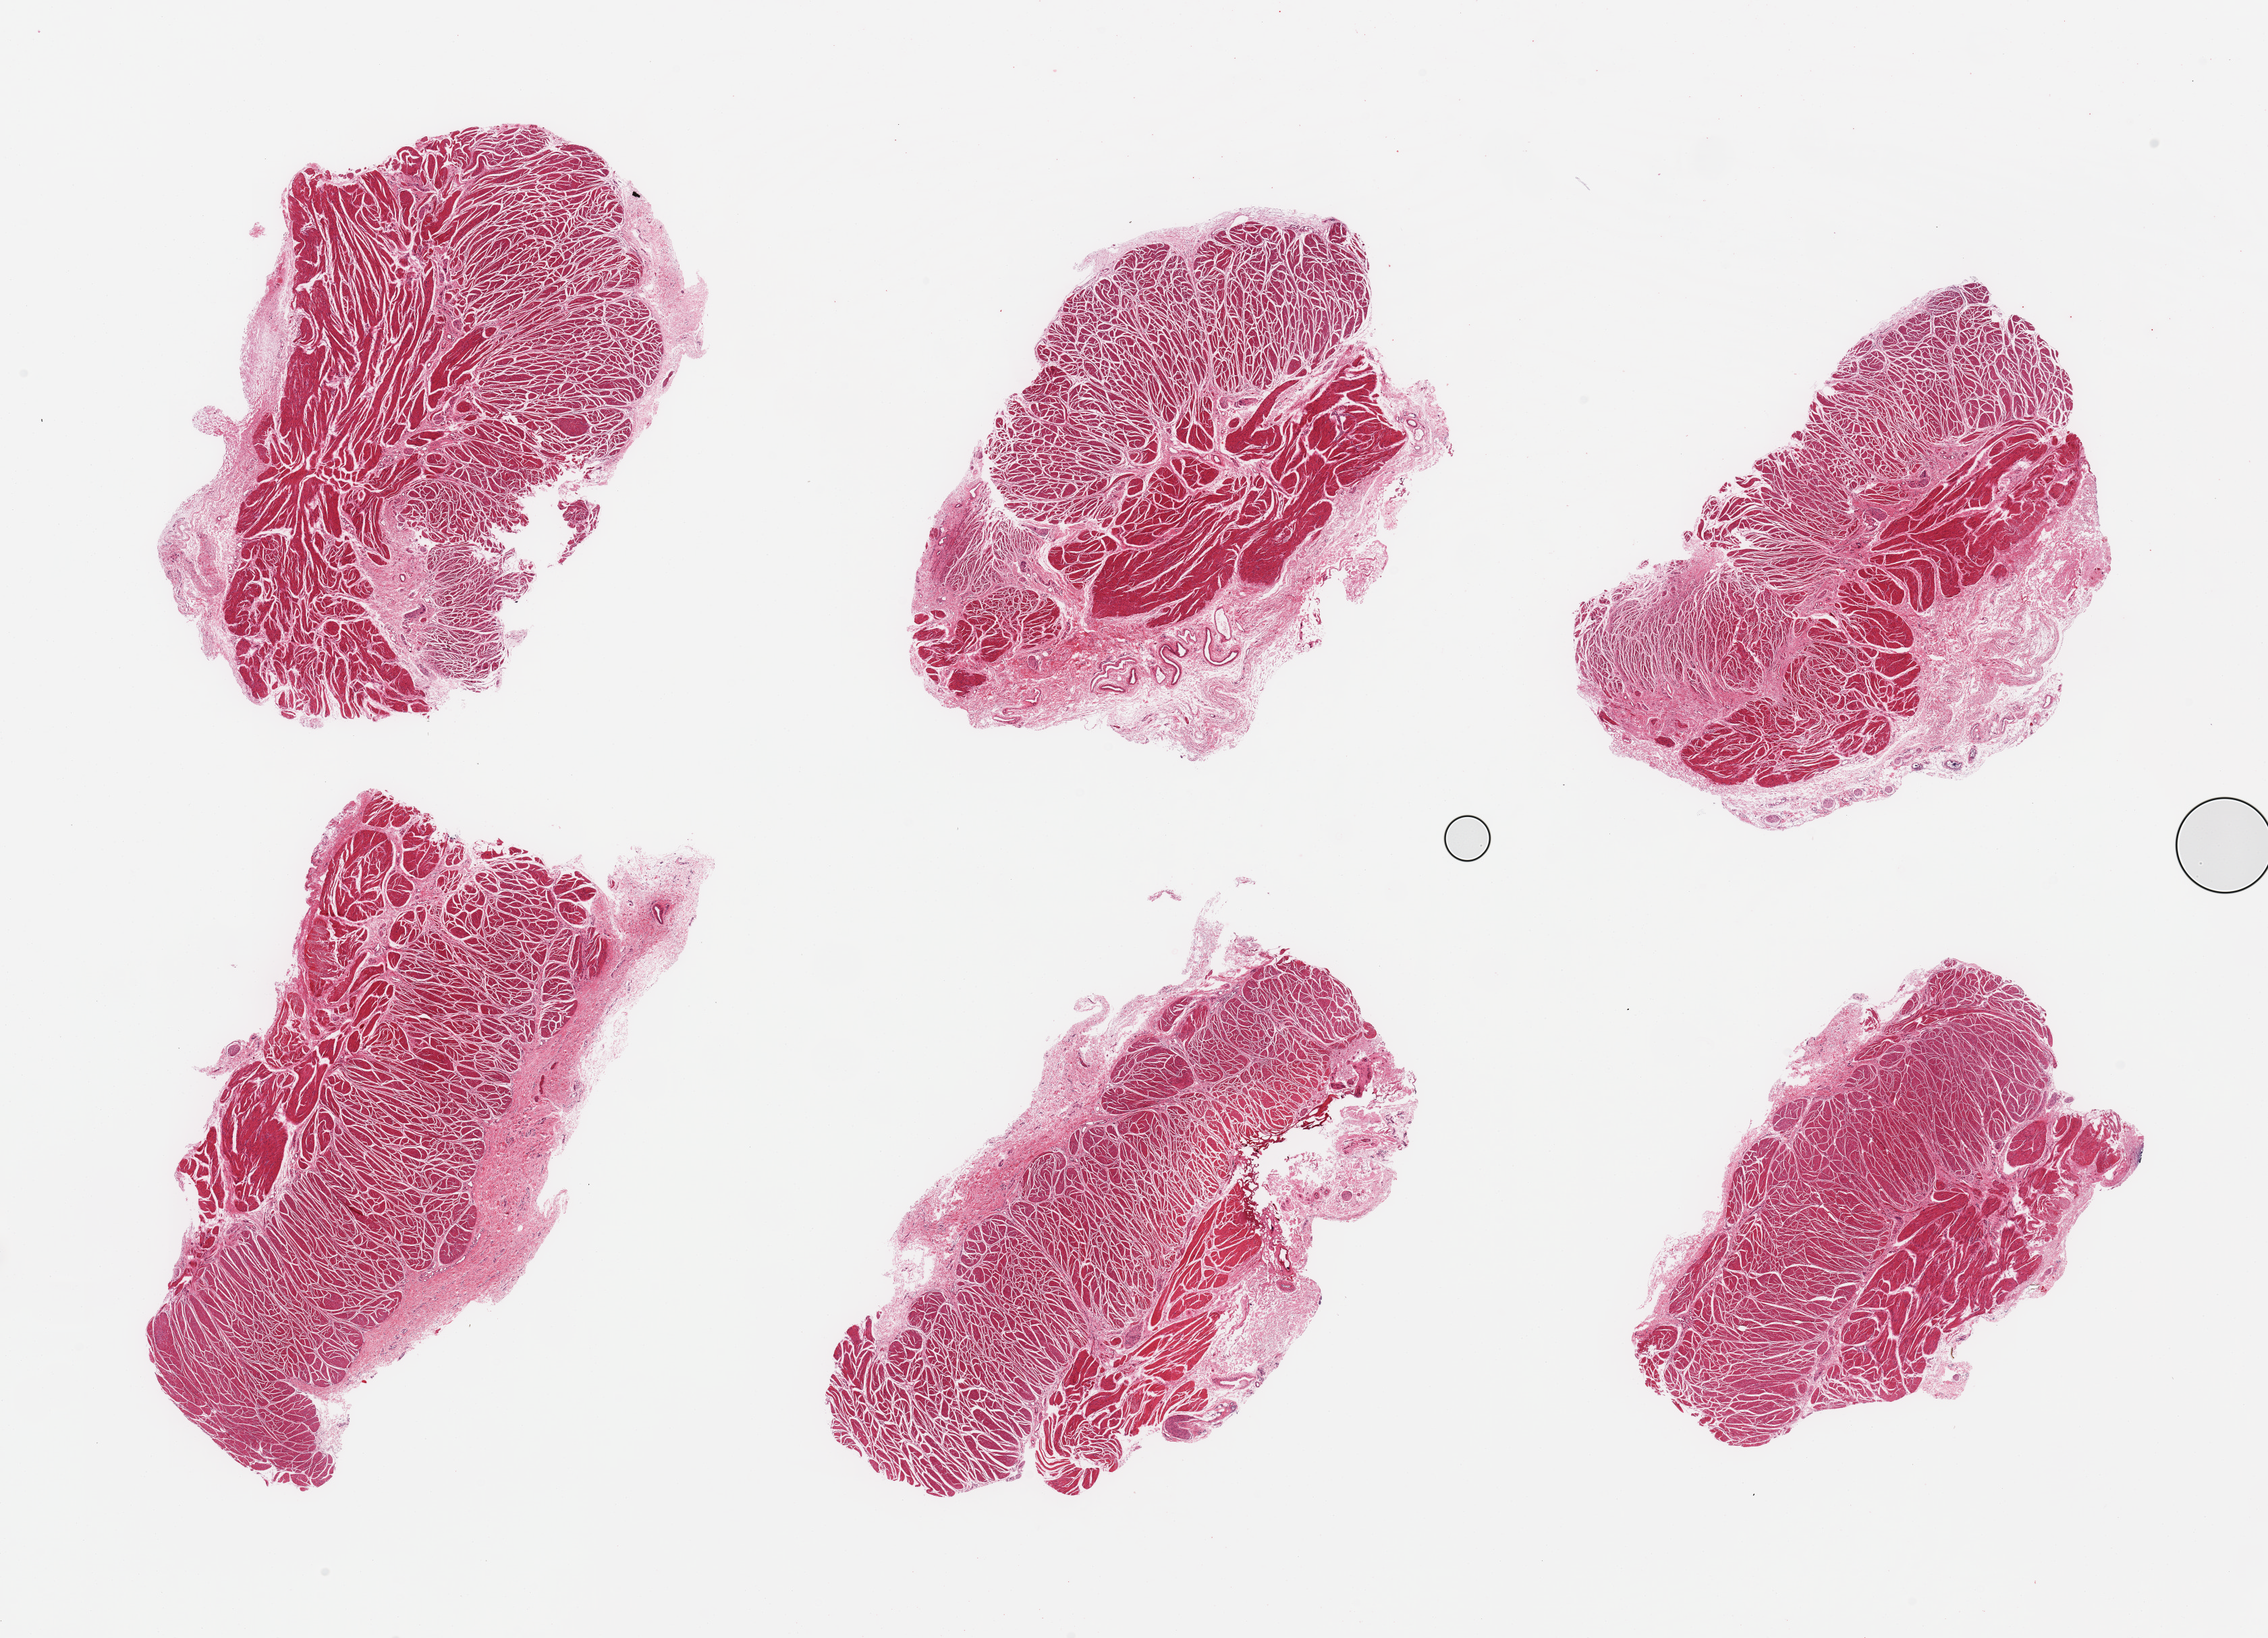
Whole-slide image, H&E stain, low-resolution overview of the scanned area, about 26.6 x 19.2 mm, PAXgene-fixed paraffin-embedded (PFPE) section, sampled site (target tissue): gastroesophageal junction, donor tissue sample.
- reviewer comment on this tissue sample: 6 pieces, confirmed target muscularis; adherent serosal nubbins up to ~1.5mm